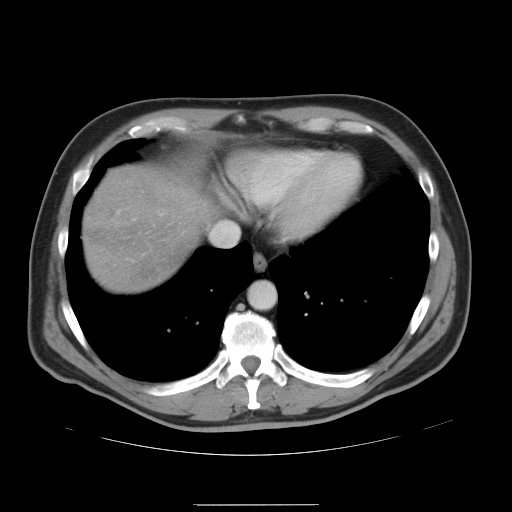
Contrast-enhanced abdominal CT, one axial slice; slice 43 of 47 in the series (ordered by position); 120 kVp; intravenous contrast given; soft-tissue window (W 400 / L 40 HU); 5 mm slice thickness; 512 × 512 image matrix. Male patient, age 61 years. From the clinical record (not read from this slice): diagnosis: colorectal cancer liver metastases, imaged before liver resection; multiple liver metastases: no.
Annotated regions visible in this slice (manually delineated by an expert):
- liver: bounding box (x1, y1, x2, y2) in pixels: (82, 153, 254, 294)
- planned liver remnant (the part of the liver to remain after resection): (83, 153, 256, 294)